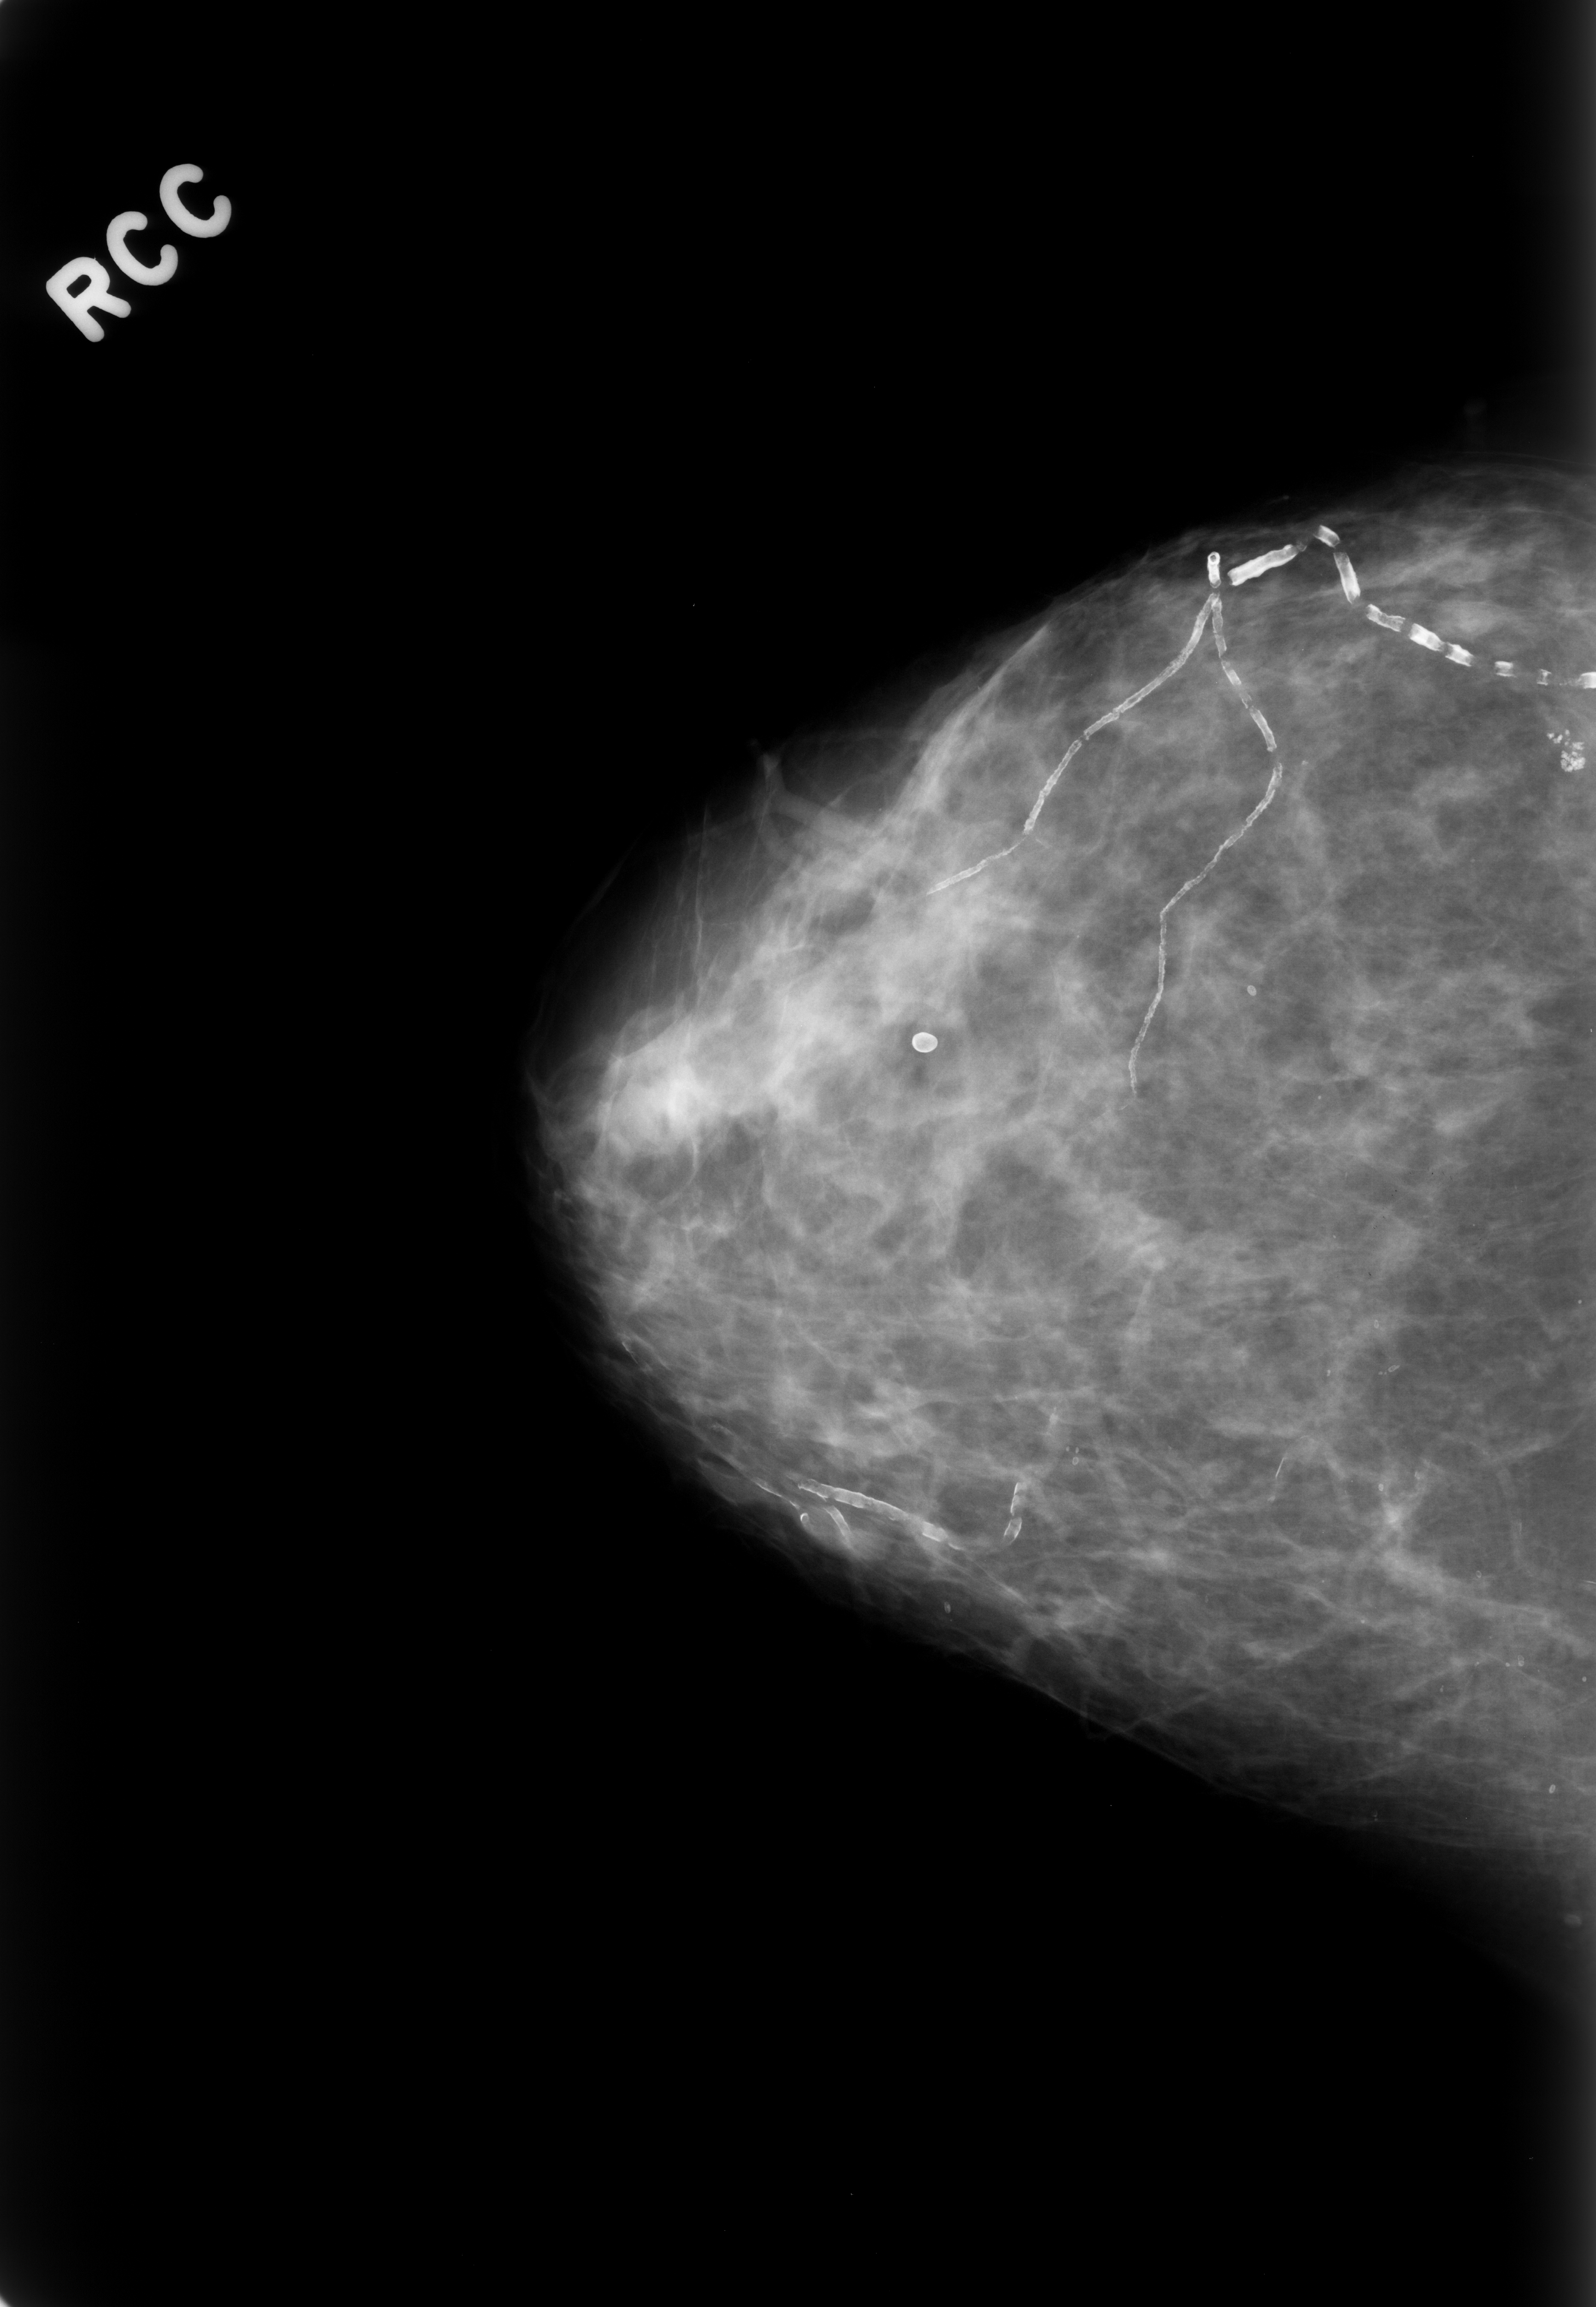
Digitized screen-film mammogram, right breast, CC view, BI-RADS breast density category 2 (scale 1–4).
- Calcifications, morphology pleomorphic, distribution clustered; BI-RADS assessment category 4; pathology result (as recorded, not read from the image): benign.